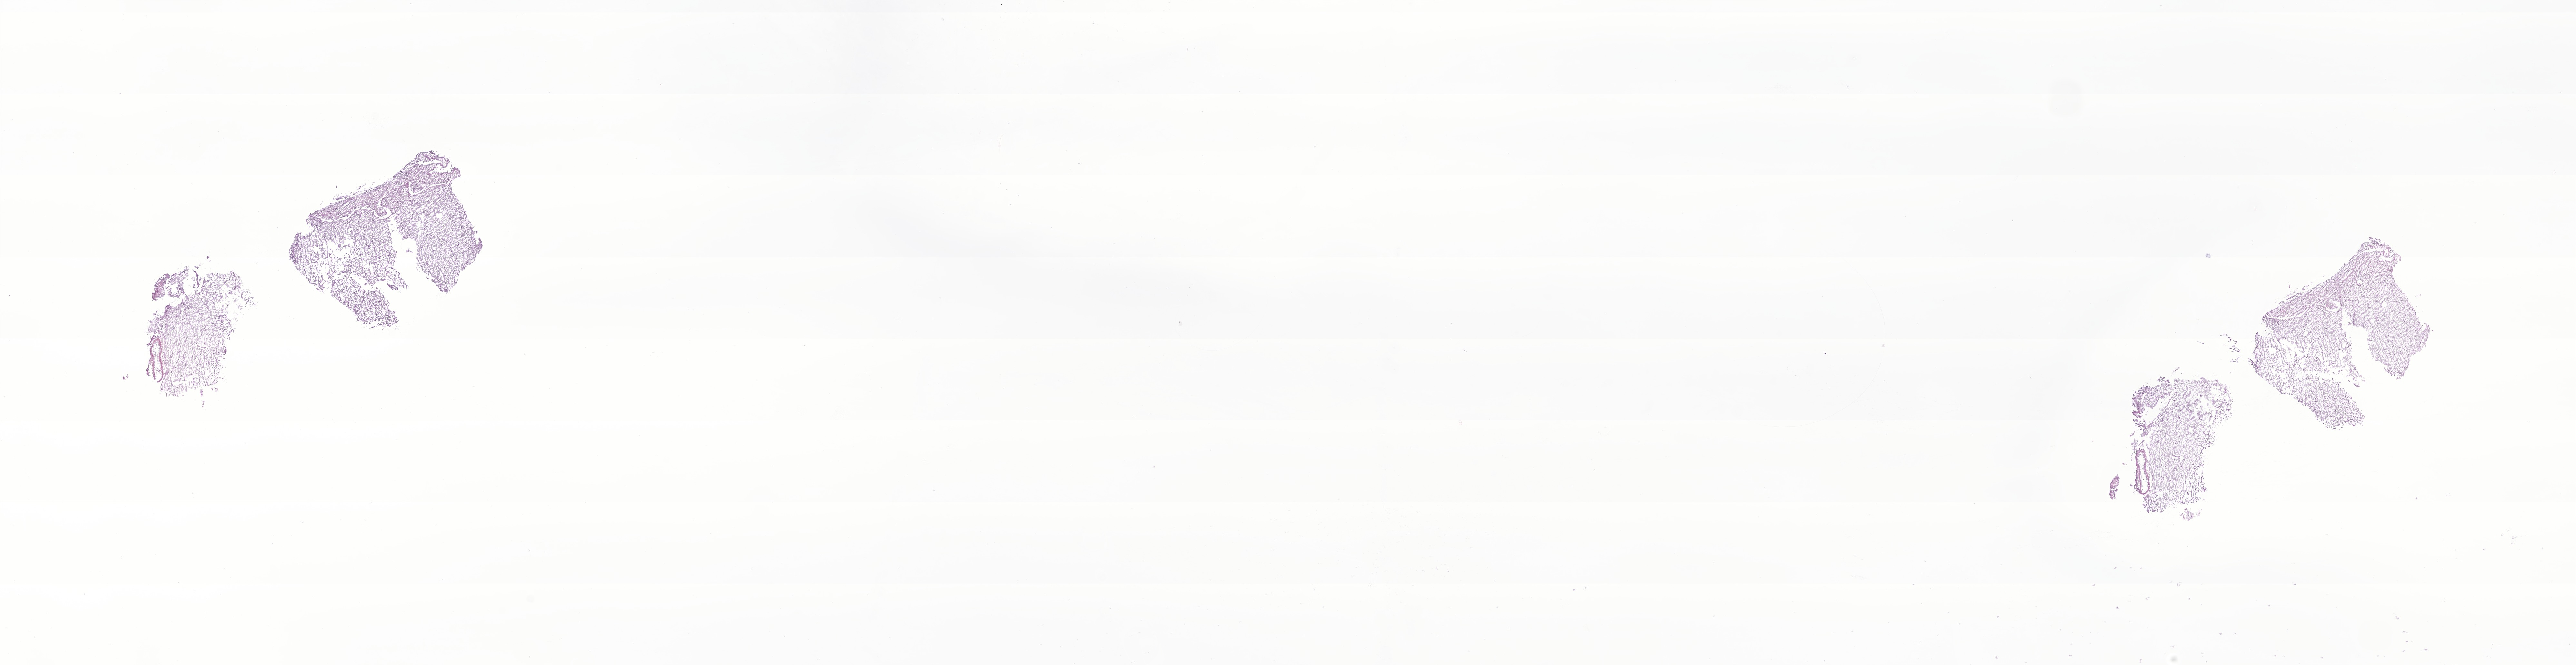
Whole-slide image, haematoxylin and eosin stain of tumor tissue from the temporal lobe, low-resolution overview of the scanned area, about 33.7 x 8.7 mm. Cryosection (OCT / tissue freezing medium). Male patient, age 137 months (11 years 5 months).
Diagnosis (ICD-O-3 morphology term): Glioma, malignant.